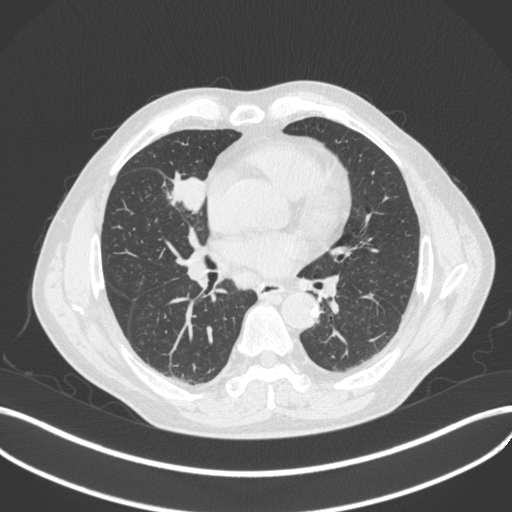
Chest CT, one axial slice; position 198 of 429 along the scan axis; 120 kVp; lung window (W 1500 / L -600 HU); 1 mm slice thickness; 512 × 512 image matrix, field of view 400 × 400 mm. Patient: male, 61 years. Case-level facts recorded for this patient, not image findings: clinical TNM (as recorded): T2b N1 M0.
Annotated regions visible in this slice (rectangle marked by the reading radiologist):
- lung tumour (recorded histology: squamous cell carcinoma): bounding box [x1, y1, x2, y2] px = [163, 170, 209, 219]